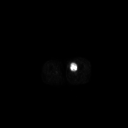
FDG PET of an extremity soft-tissue mass (from a PET/CT study), one axial slice; slice 220 of 267 in the series (ordered by position); 128 × 128 image matrix, field of view 700 × 700 mm. Patient: male, 48 years. From the clinical record (not read from this slice): histological type: pleiomorphic leiomyosarcoma; grade: high; site of the primary tumour: left thigh.
Annotated regions visible in this slice (expert contour drawn on MRI and transferred to this co-registered scan by the dataset authors):
- gross tumour volume including surrounding oedema: box from (x=69, y=62) to (x=78, y=72) px
- gross tumour volume (mass): (x=69, y=62)–(x=77, y=72)